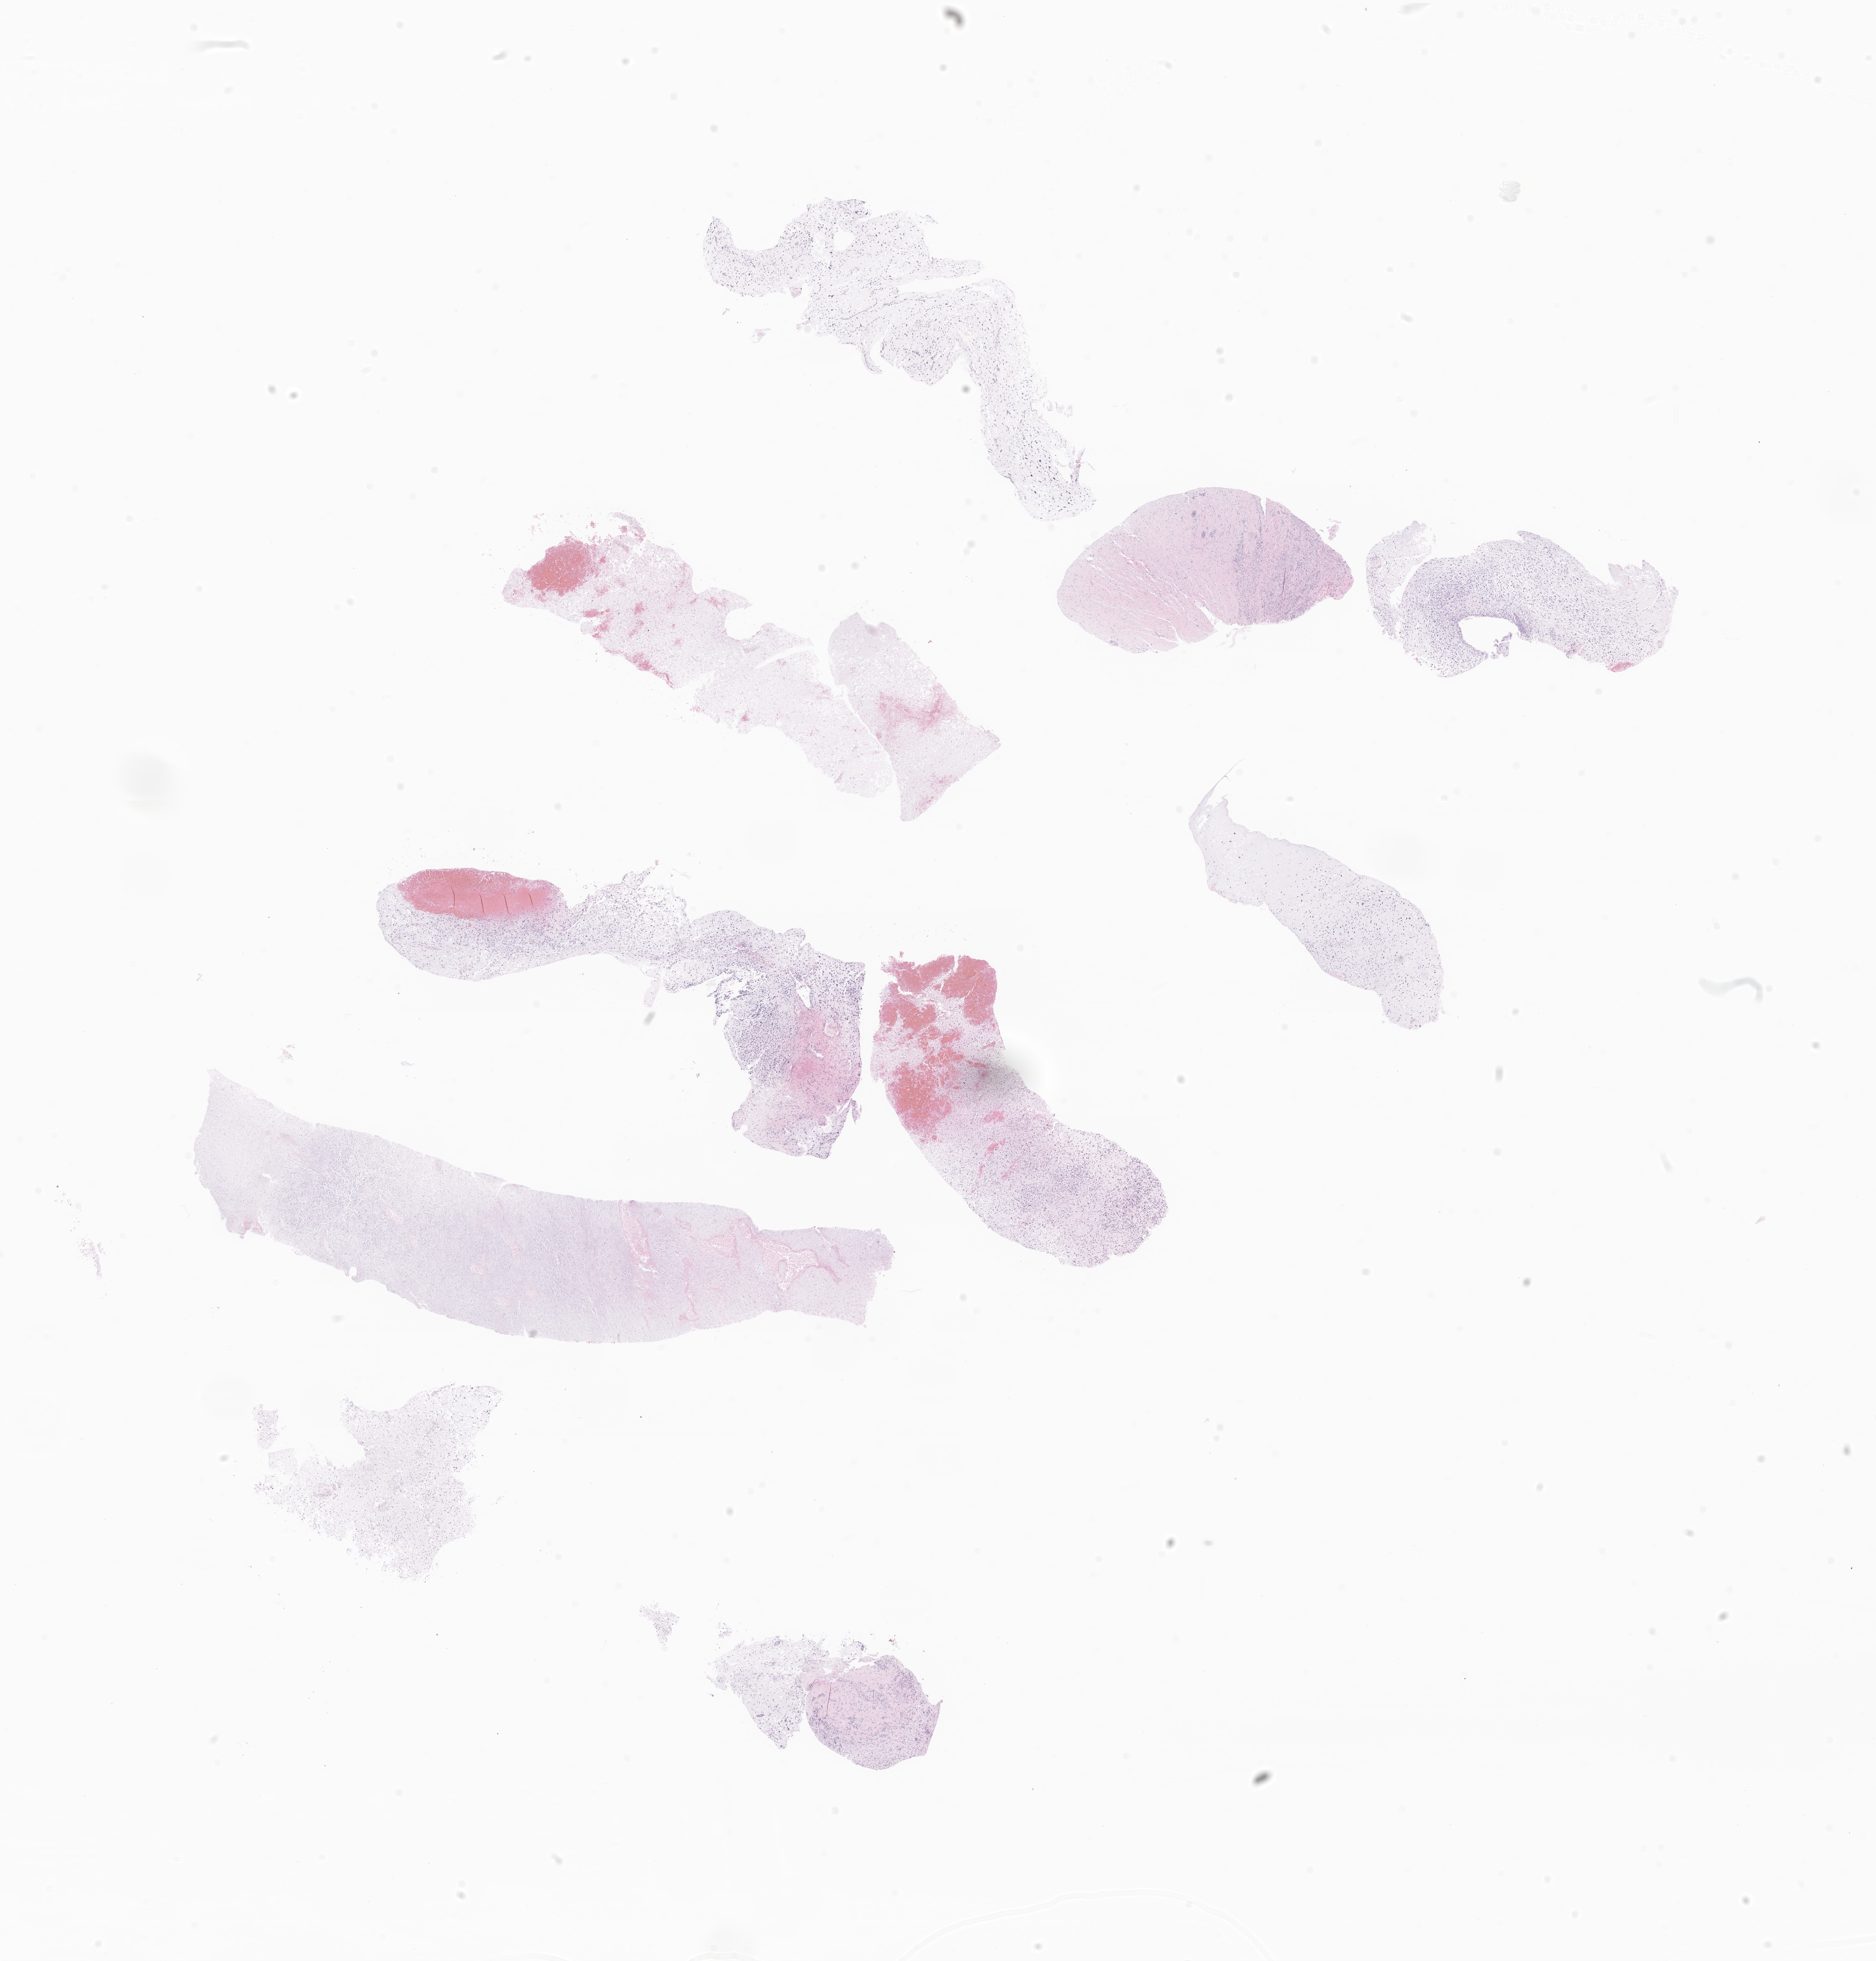
Haematoxylin and eosin whole-slide image of tumor tissue from the liver — whole scanned area (about 18.9 x 19.8 mm) shown as a low-resolution overview; formalin-fixed, paraffin-embedded (FFPE) tissue. Patient: female, age 151 months (12 years 7 months).
Diagnosis (ICD-O-3 morphology term): Embryonal sarcoma.